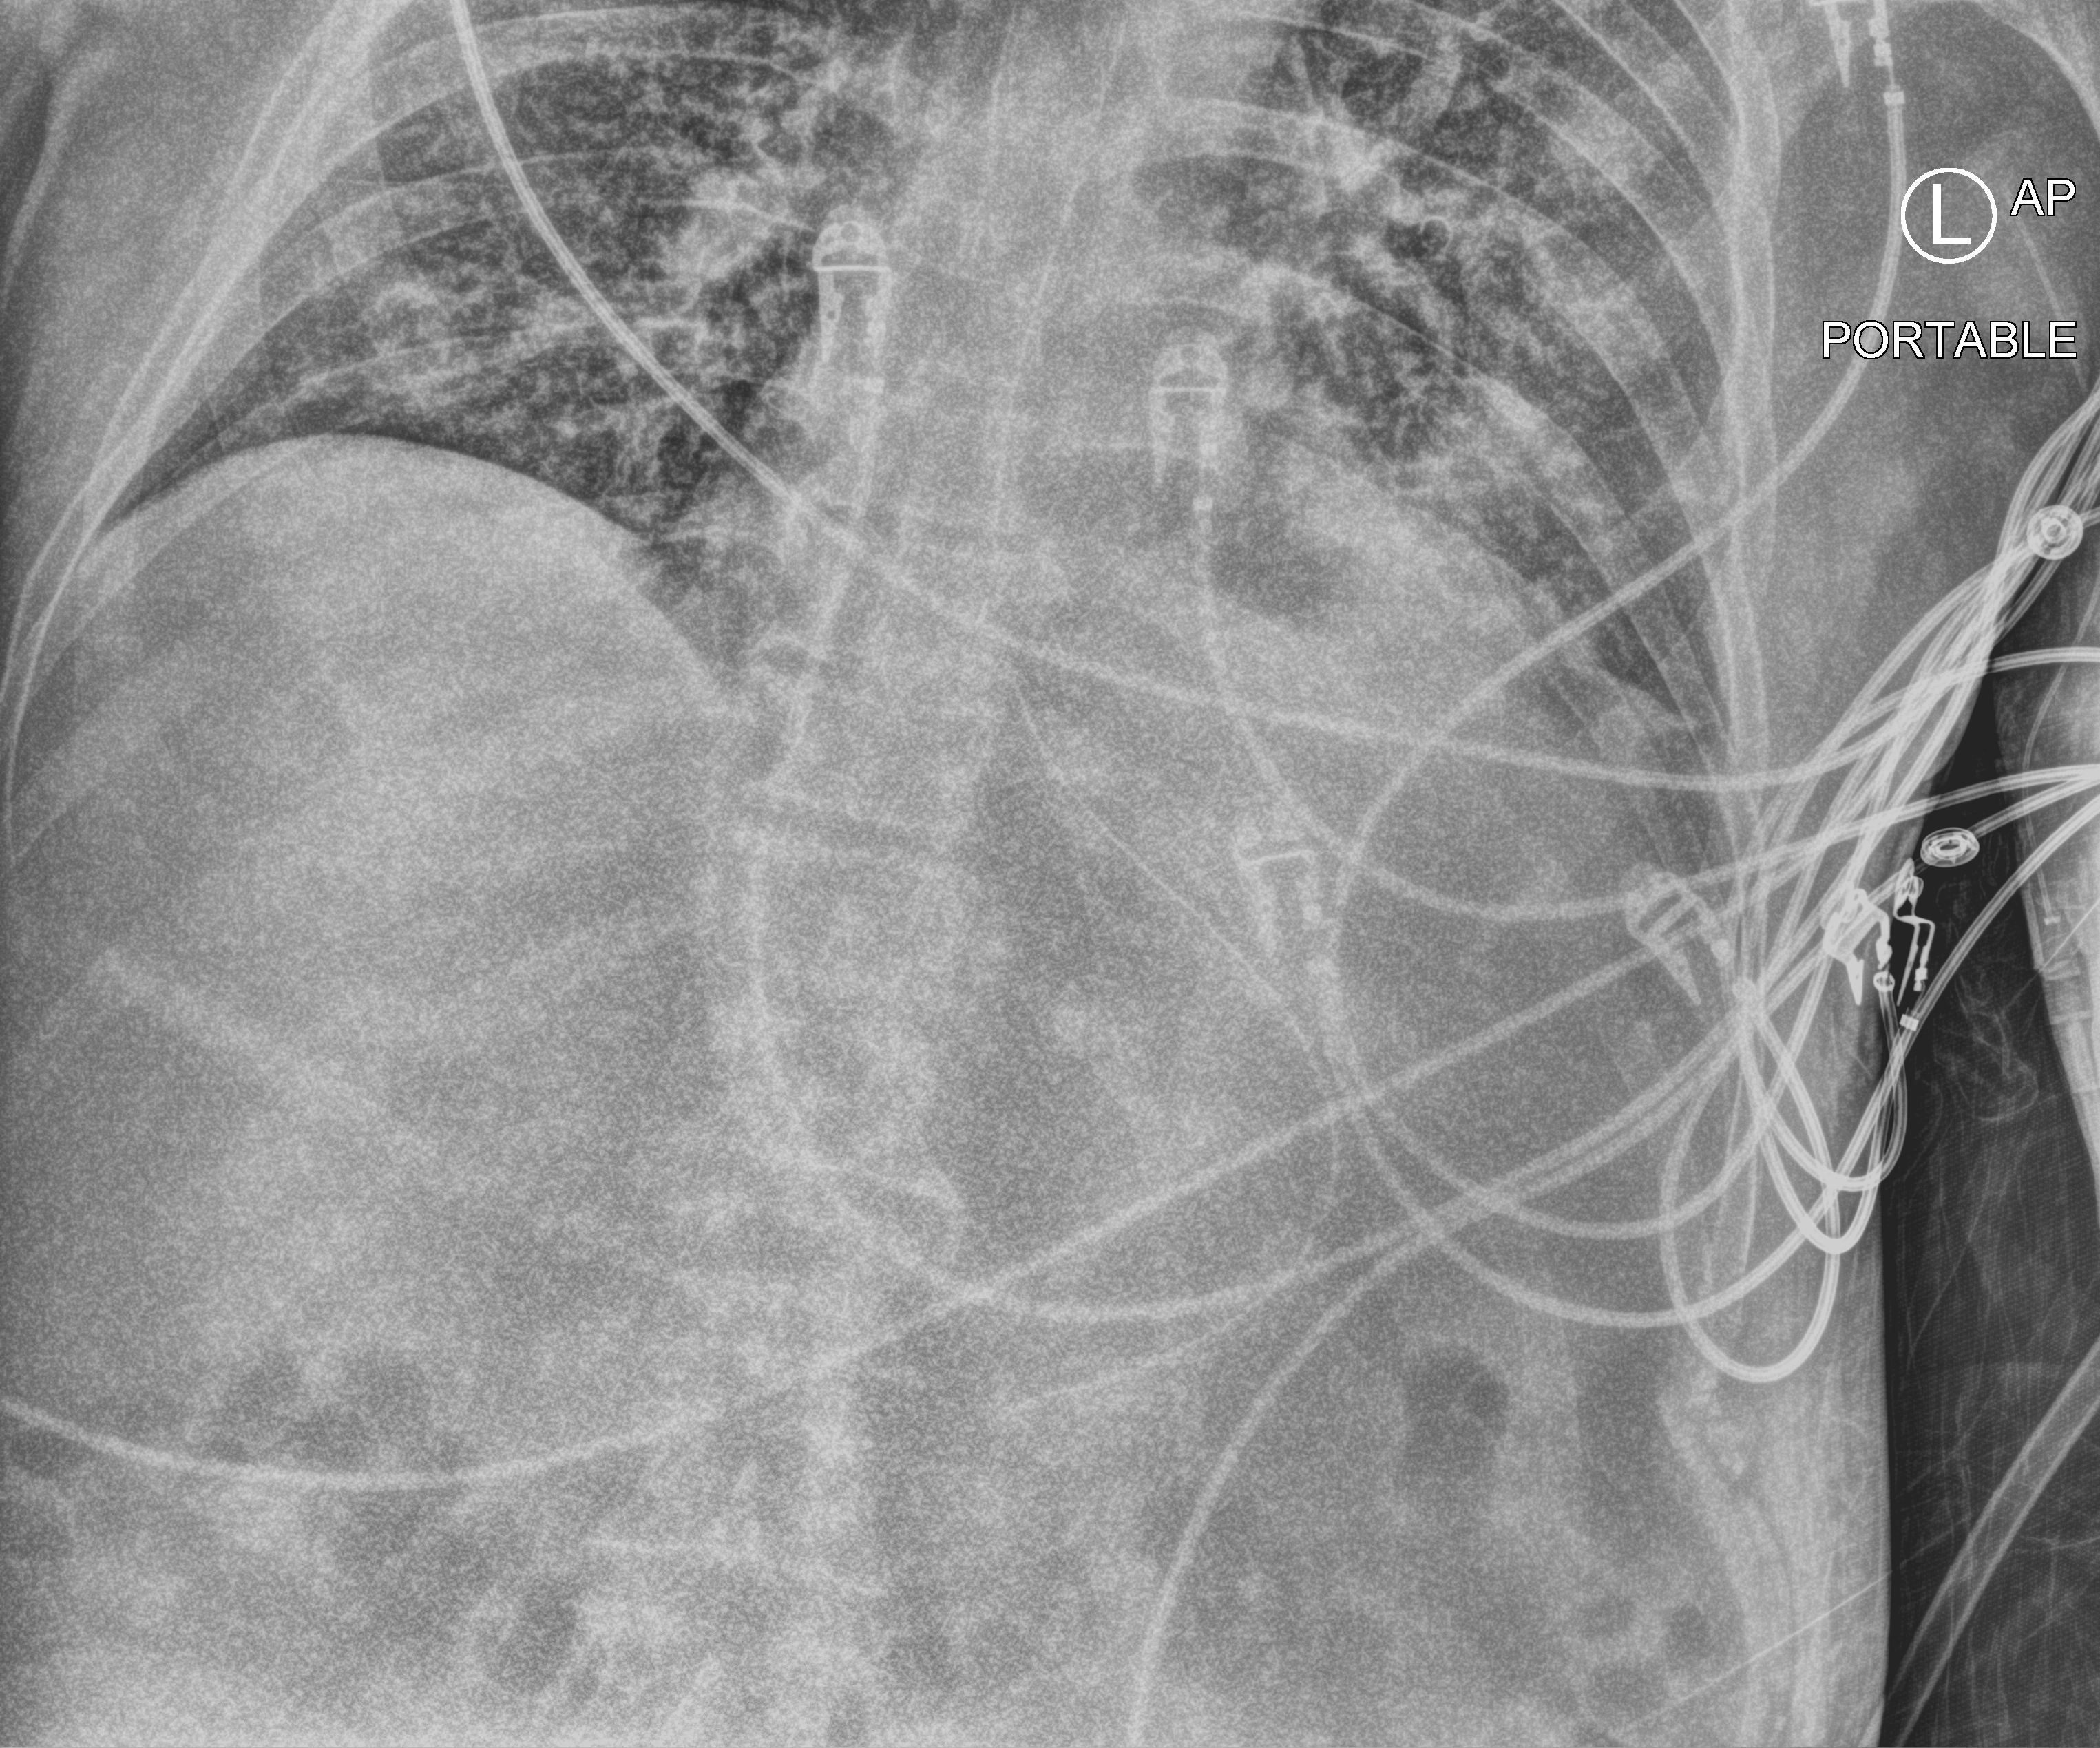
Chest X-ray (portable). Patient hospitalised with COVID-19; male, aged 18–59 years.
From the hospital-stay record, not from the radiograph (when in the stay this image was taken is not recorded):
- admitted to intensive care during this hospital stay: no
- mechanically ventilated during this hospital stay: yes
- length of hospital stay: 19 days